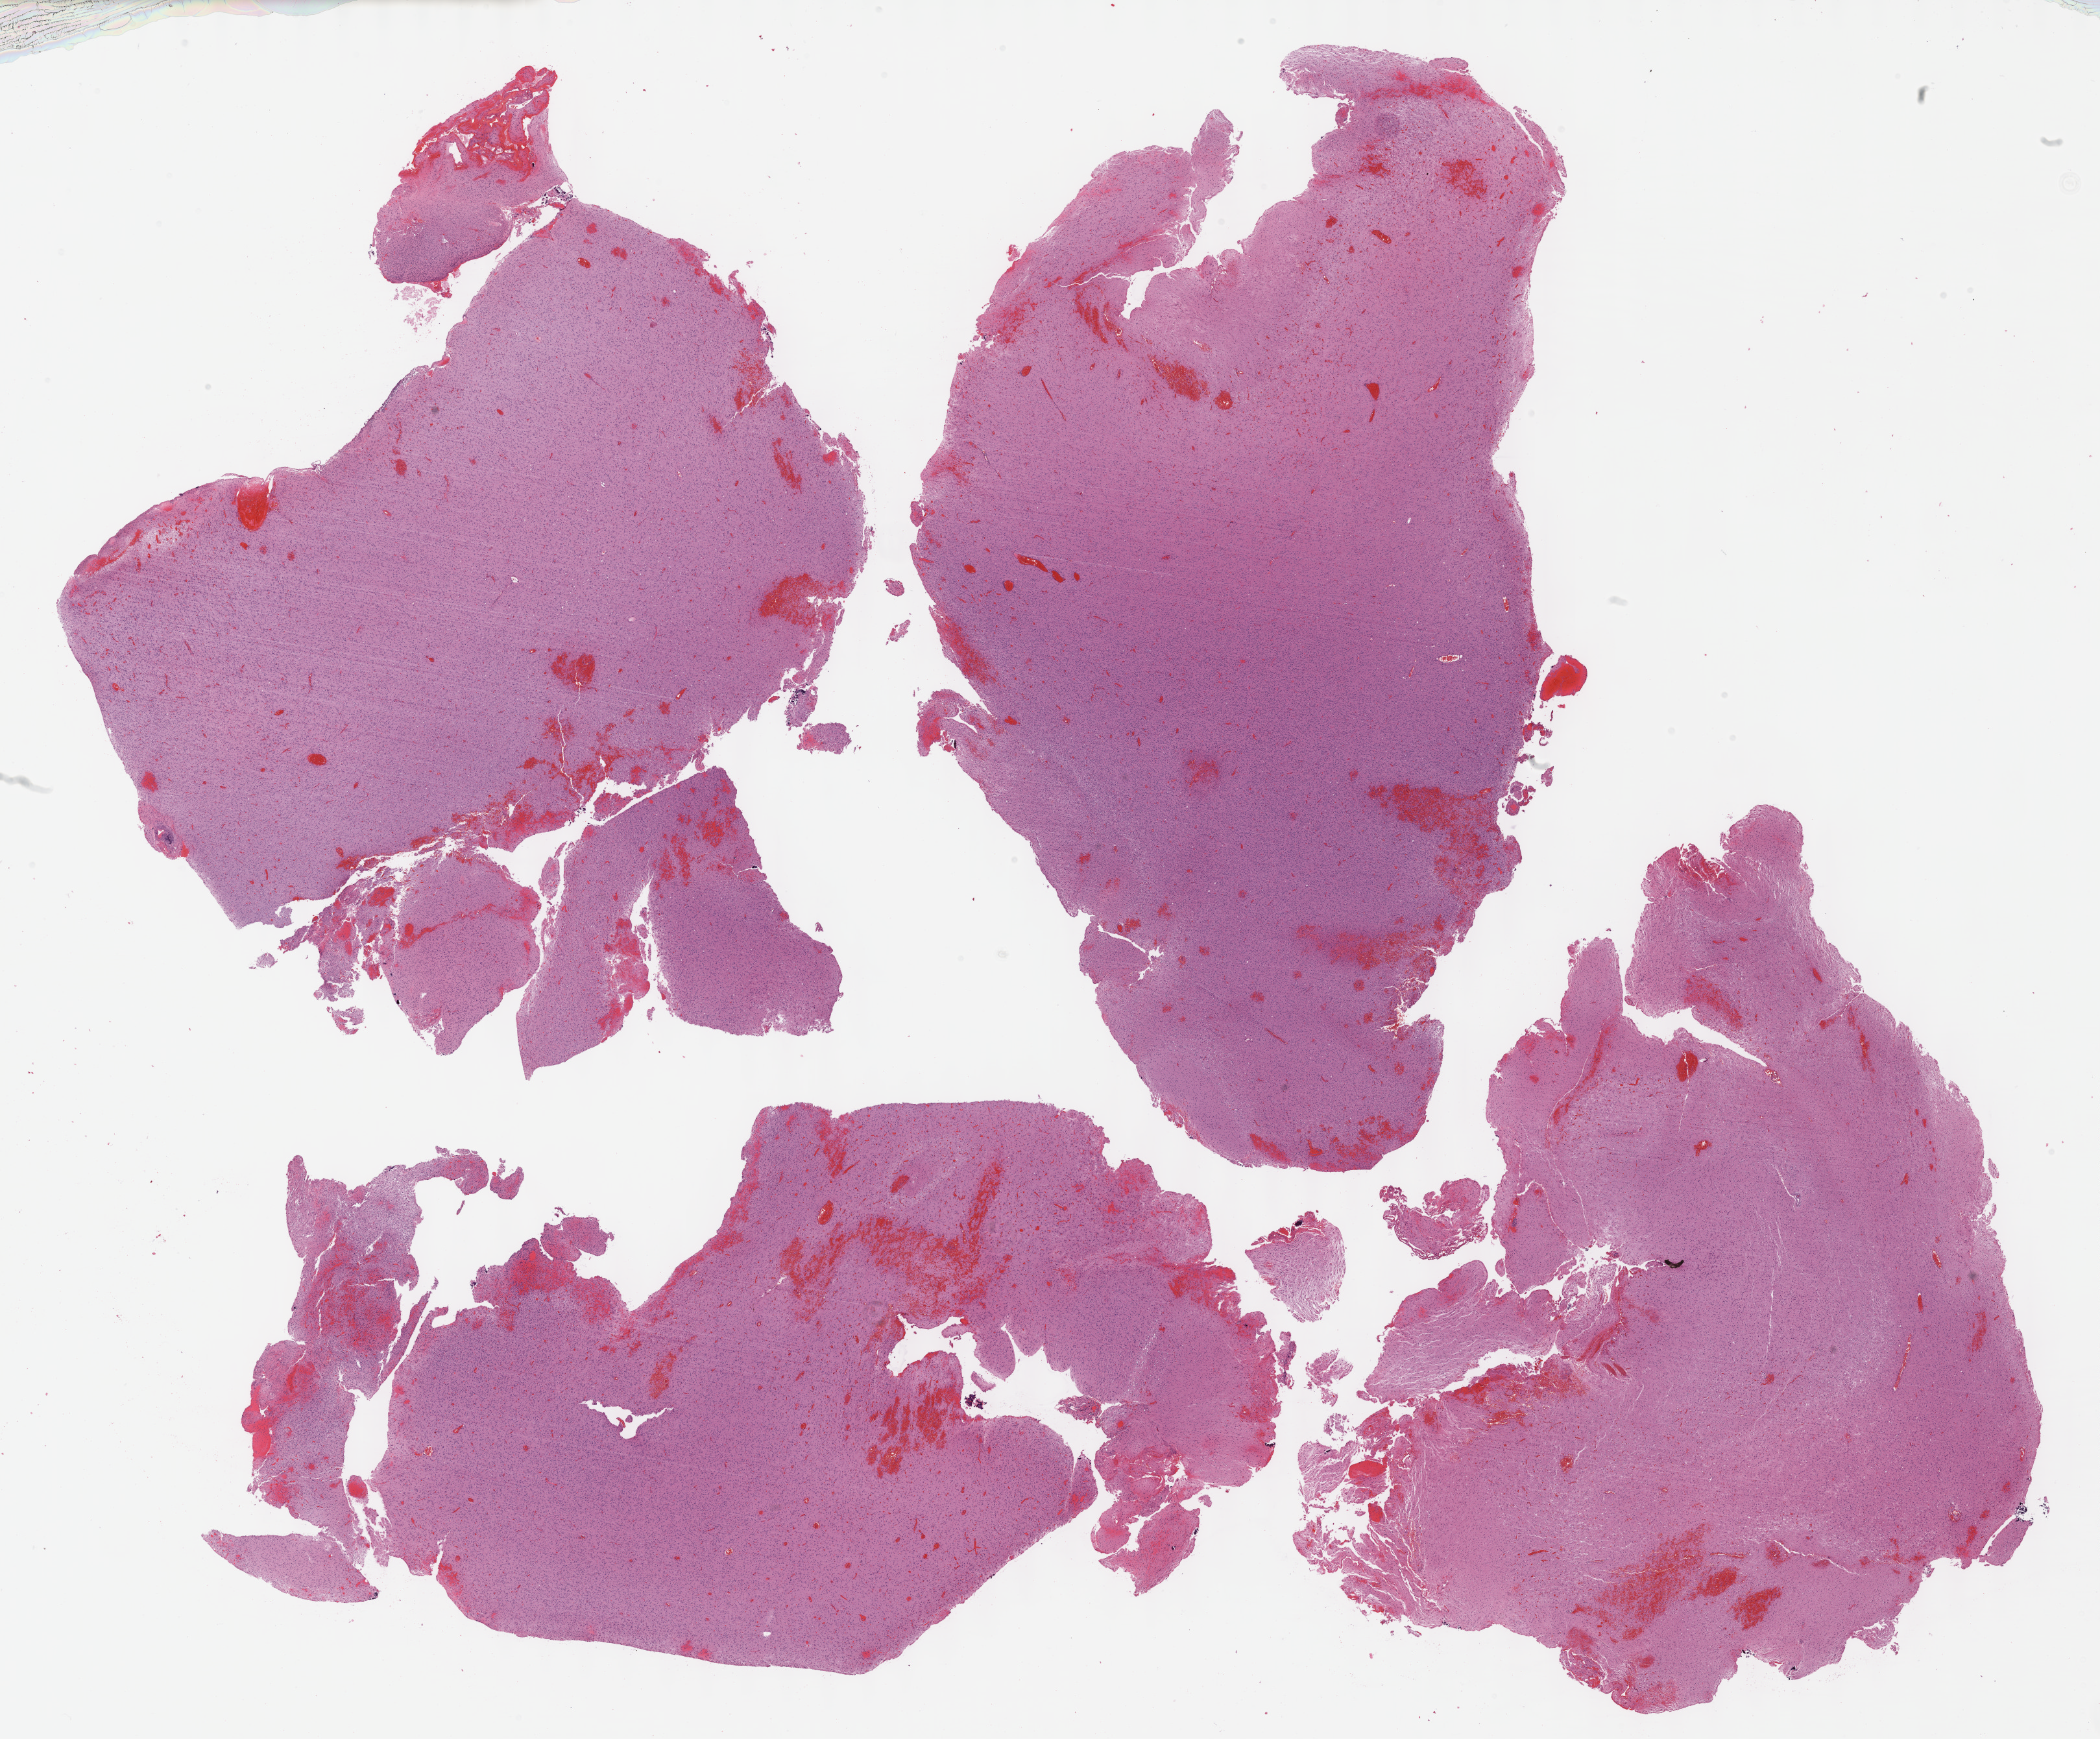
Whole-slide histology image, H&E — a low-resolution overview of the entire scanned area, about 26.2 x 21.7 mm, formalin-fixed paraffin-embedded (FFPE) diagnostic section, brain, primary tumour sample. Male patient; age at initial diagnosis 57 years. Histologic grade: G3 (poorly differentiated).
Histologic diagnosis: Astrocytoma, anaplastic (cerebrum).